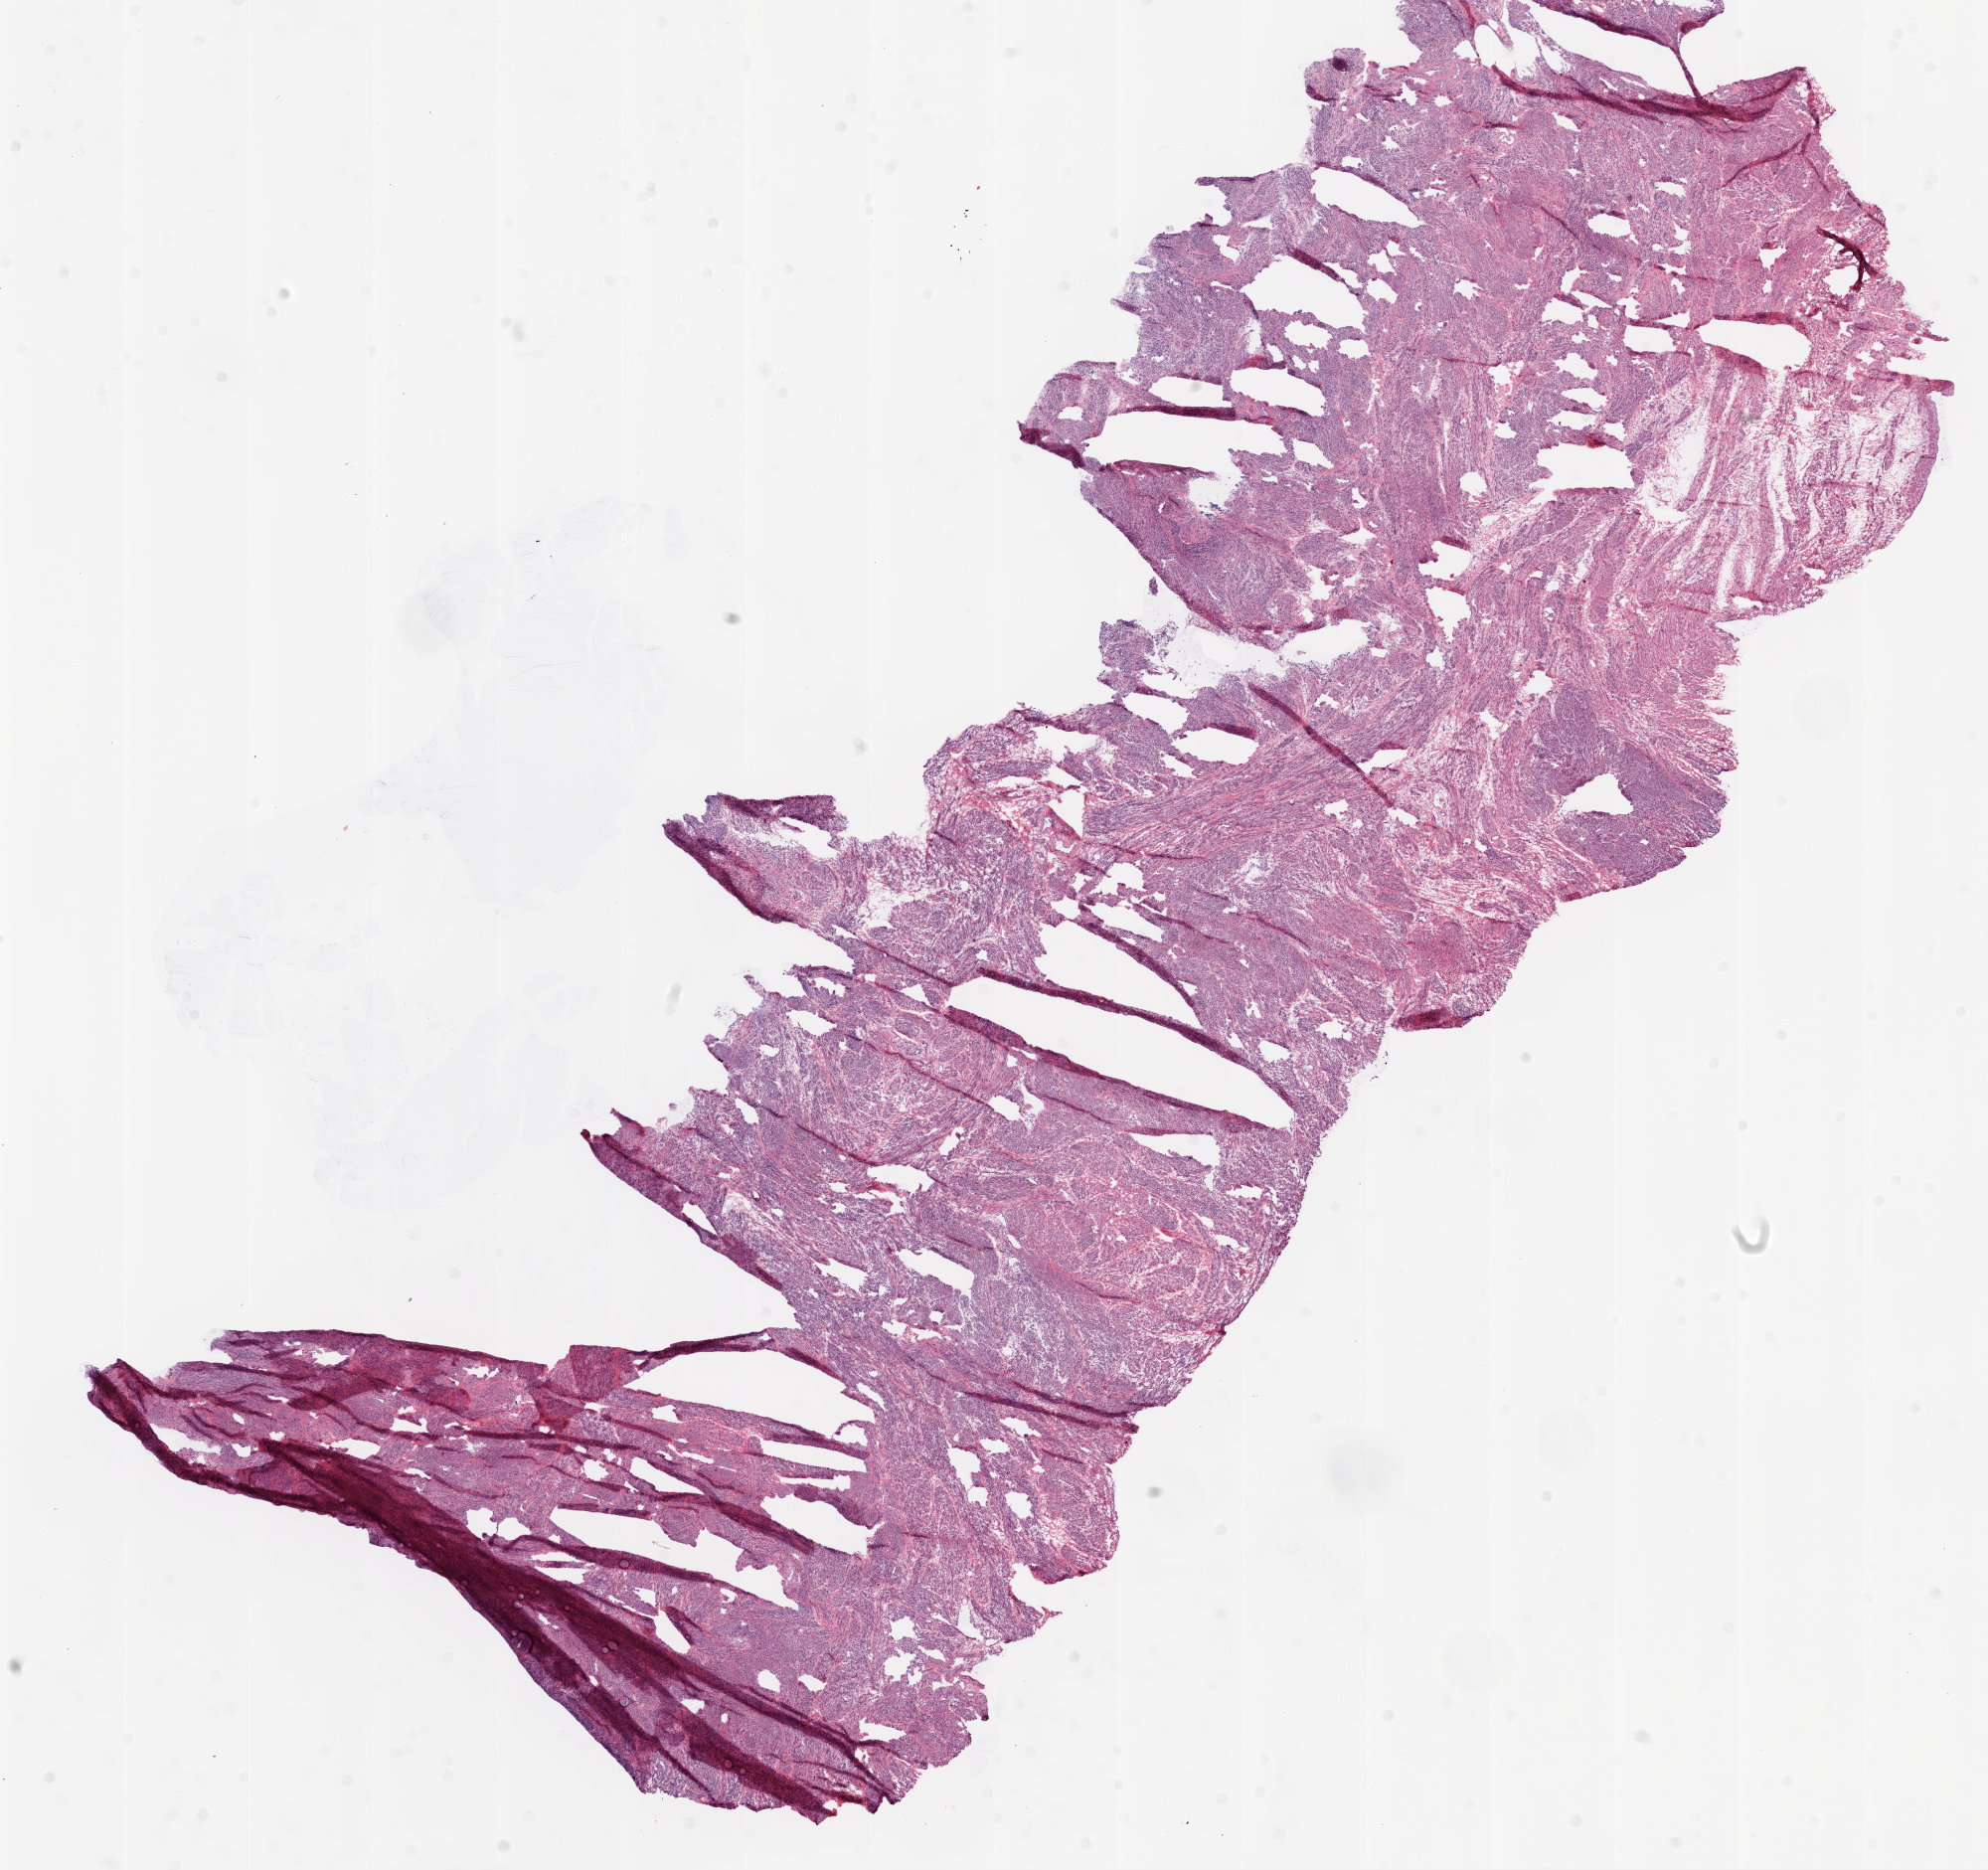
Digitized H&E tissue section (whole slide), whole scanned area (about 16.0 x 15.1 mm, from a 20x scan) shown as a low-resolution overview; frozen section from the bottom of the tissue portion; solid tissue normal (non-tumour tissue) sample from the ovary. Female, age 69 years at initial diagnosis.
* this section: solid tissue normal sample (biorepository sample class)
* patient diagnosis: Serous cystadenocarcinoma, NOS